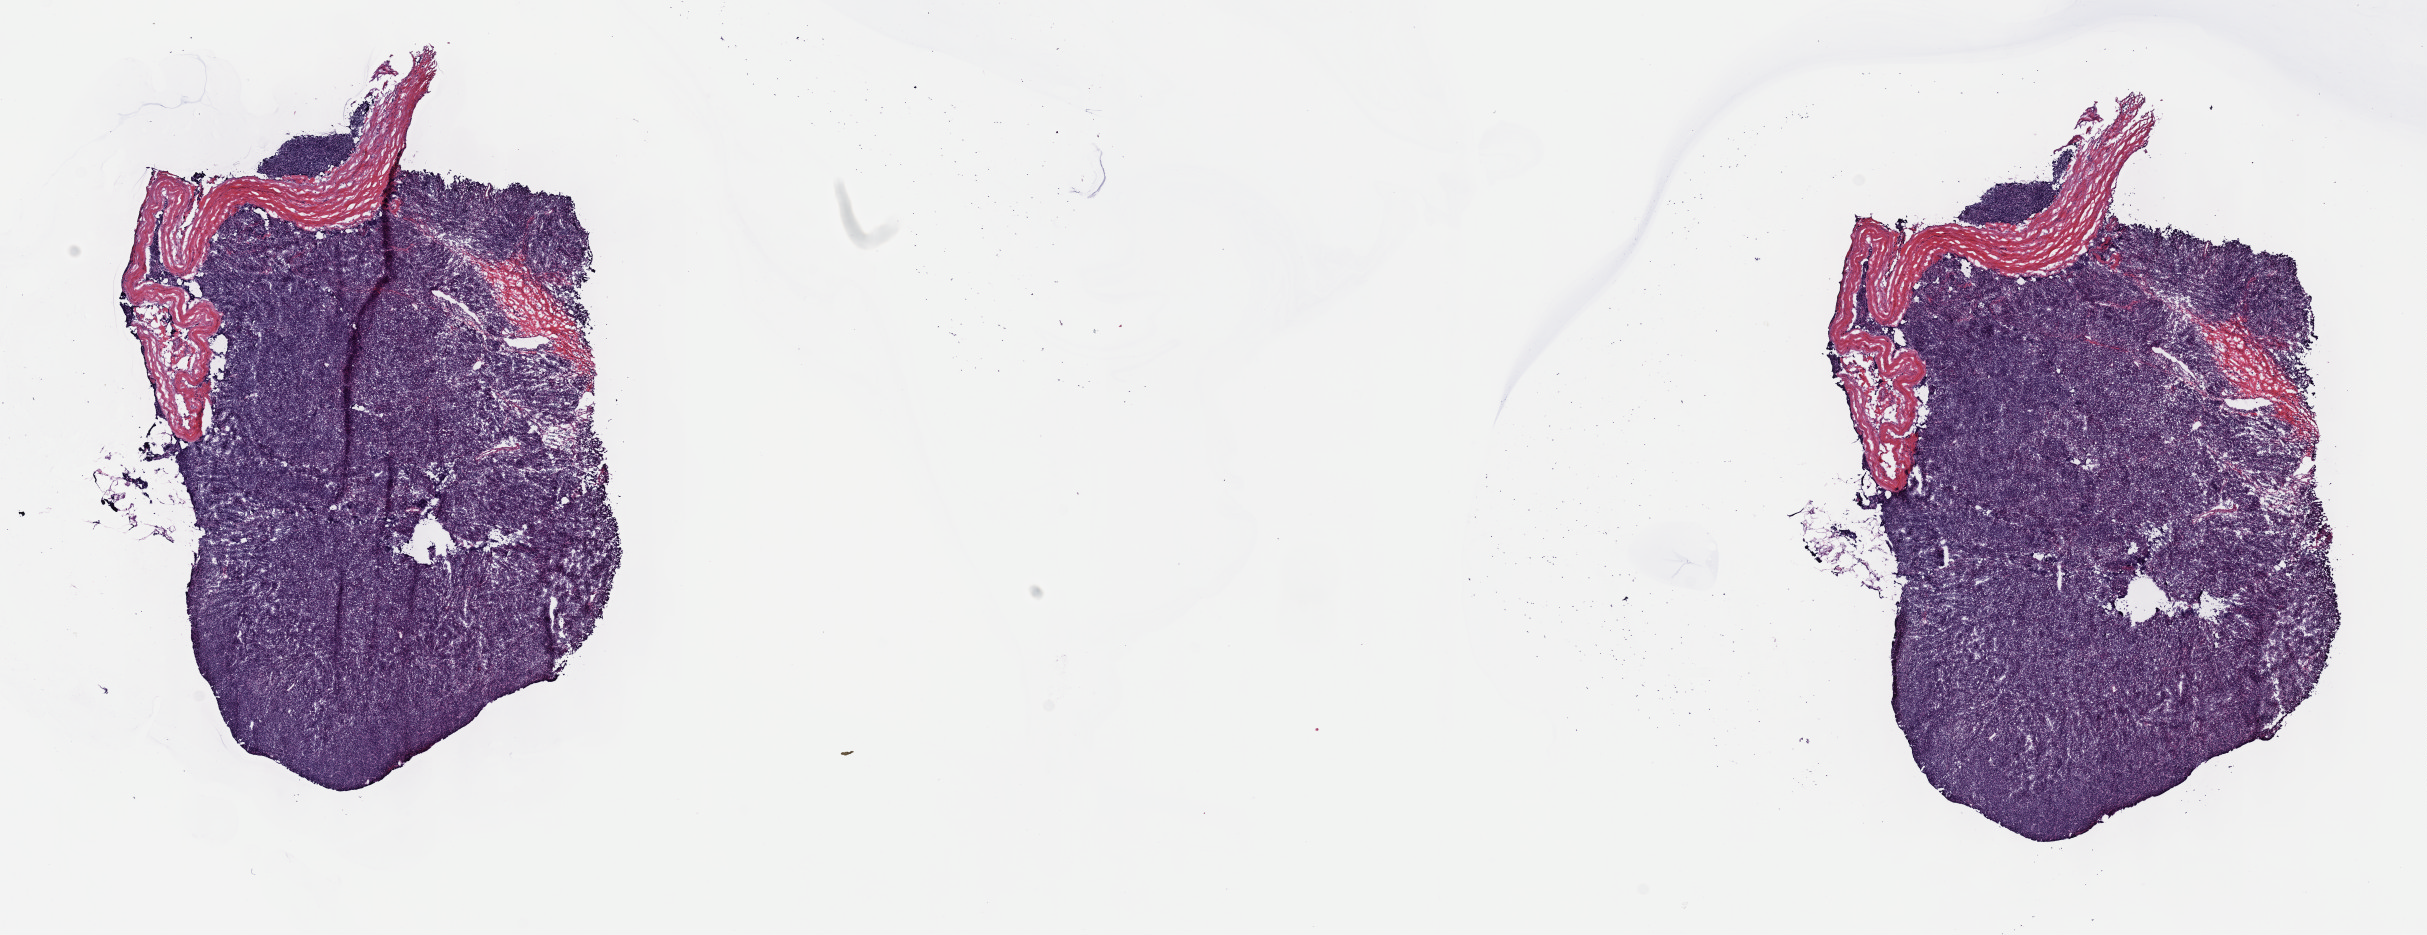
H&E-stained whole-slide image — a low-resolution overview of the entire scanned area, about 19.6 x 7.6 mm. Frozen section. Primary tumour sample from the thymus. Male patient; age at initial diagnosis 62 years. Pathologist review of this section (percent, as recorded): tumour cells 95%, tumour nuclei 95%, normal cells 0%, stromal cells 5%, necrosis 0%. Infiltration values recorded for this section: lymphocyte infiltration 0%, monocyte infiltration 0%, neutrophil infiltration 0%.
• pathologic diagnosis: Thymoma, type AB, malignant